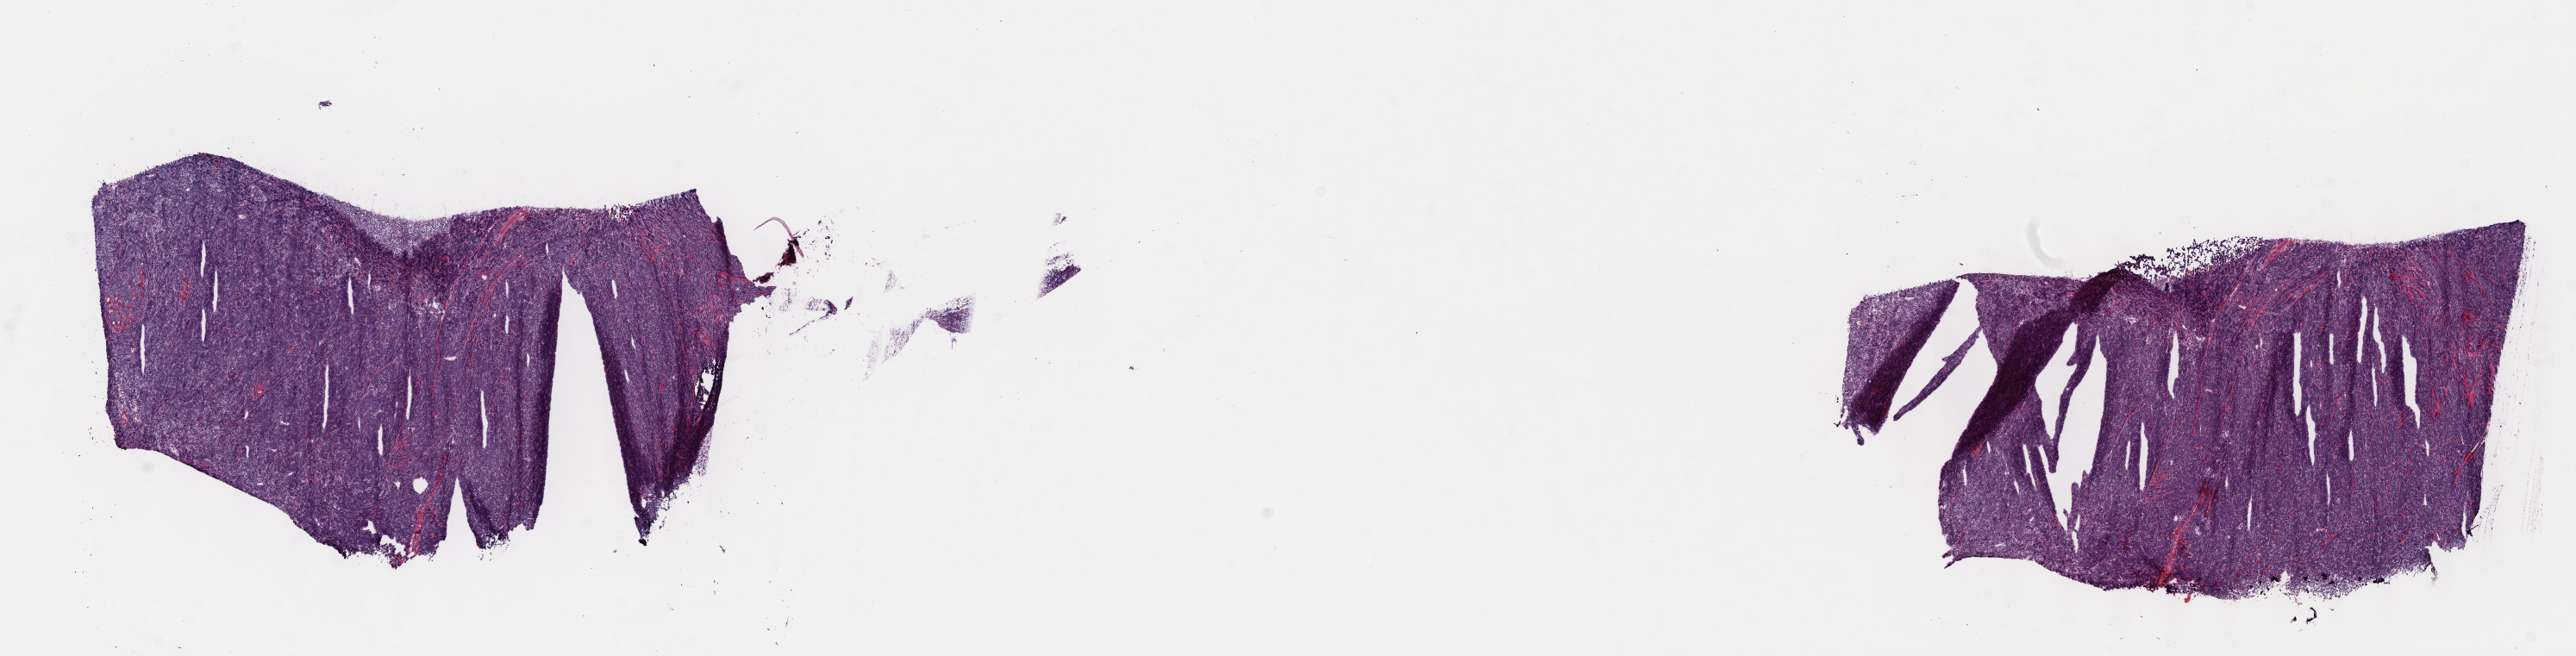
Digitized H&E-stained section — shown as a low-resolution overview of the whole scanned area (about 24.1 x 6.1 mm), cryosection, primary tumor, site: cranium. Male patient, age 11 years. Pathologist review of this section (percent, as recorded): tumor cells 90%, tumor nuclei 90%, stromal cells 10%, necrosis 0%, normal cells 0%. Infiltration values recorded for this section: lymphocyte infiltration 10%, monocyte infiltration 10%, neutrophil infiltration 0%.
• section: bottom of the tissue portion
• Ann Arbor stage (patient): Stage I
• diagnosis: Burkitt lymphoma, NOS